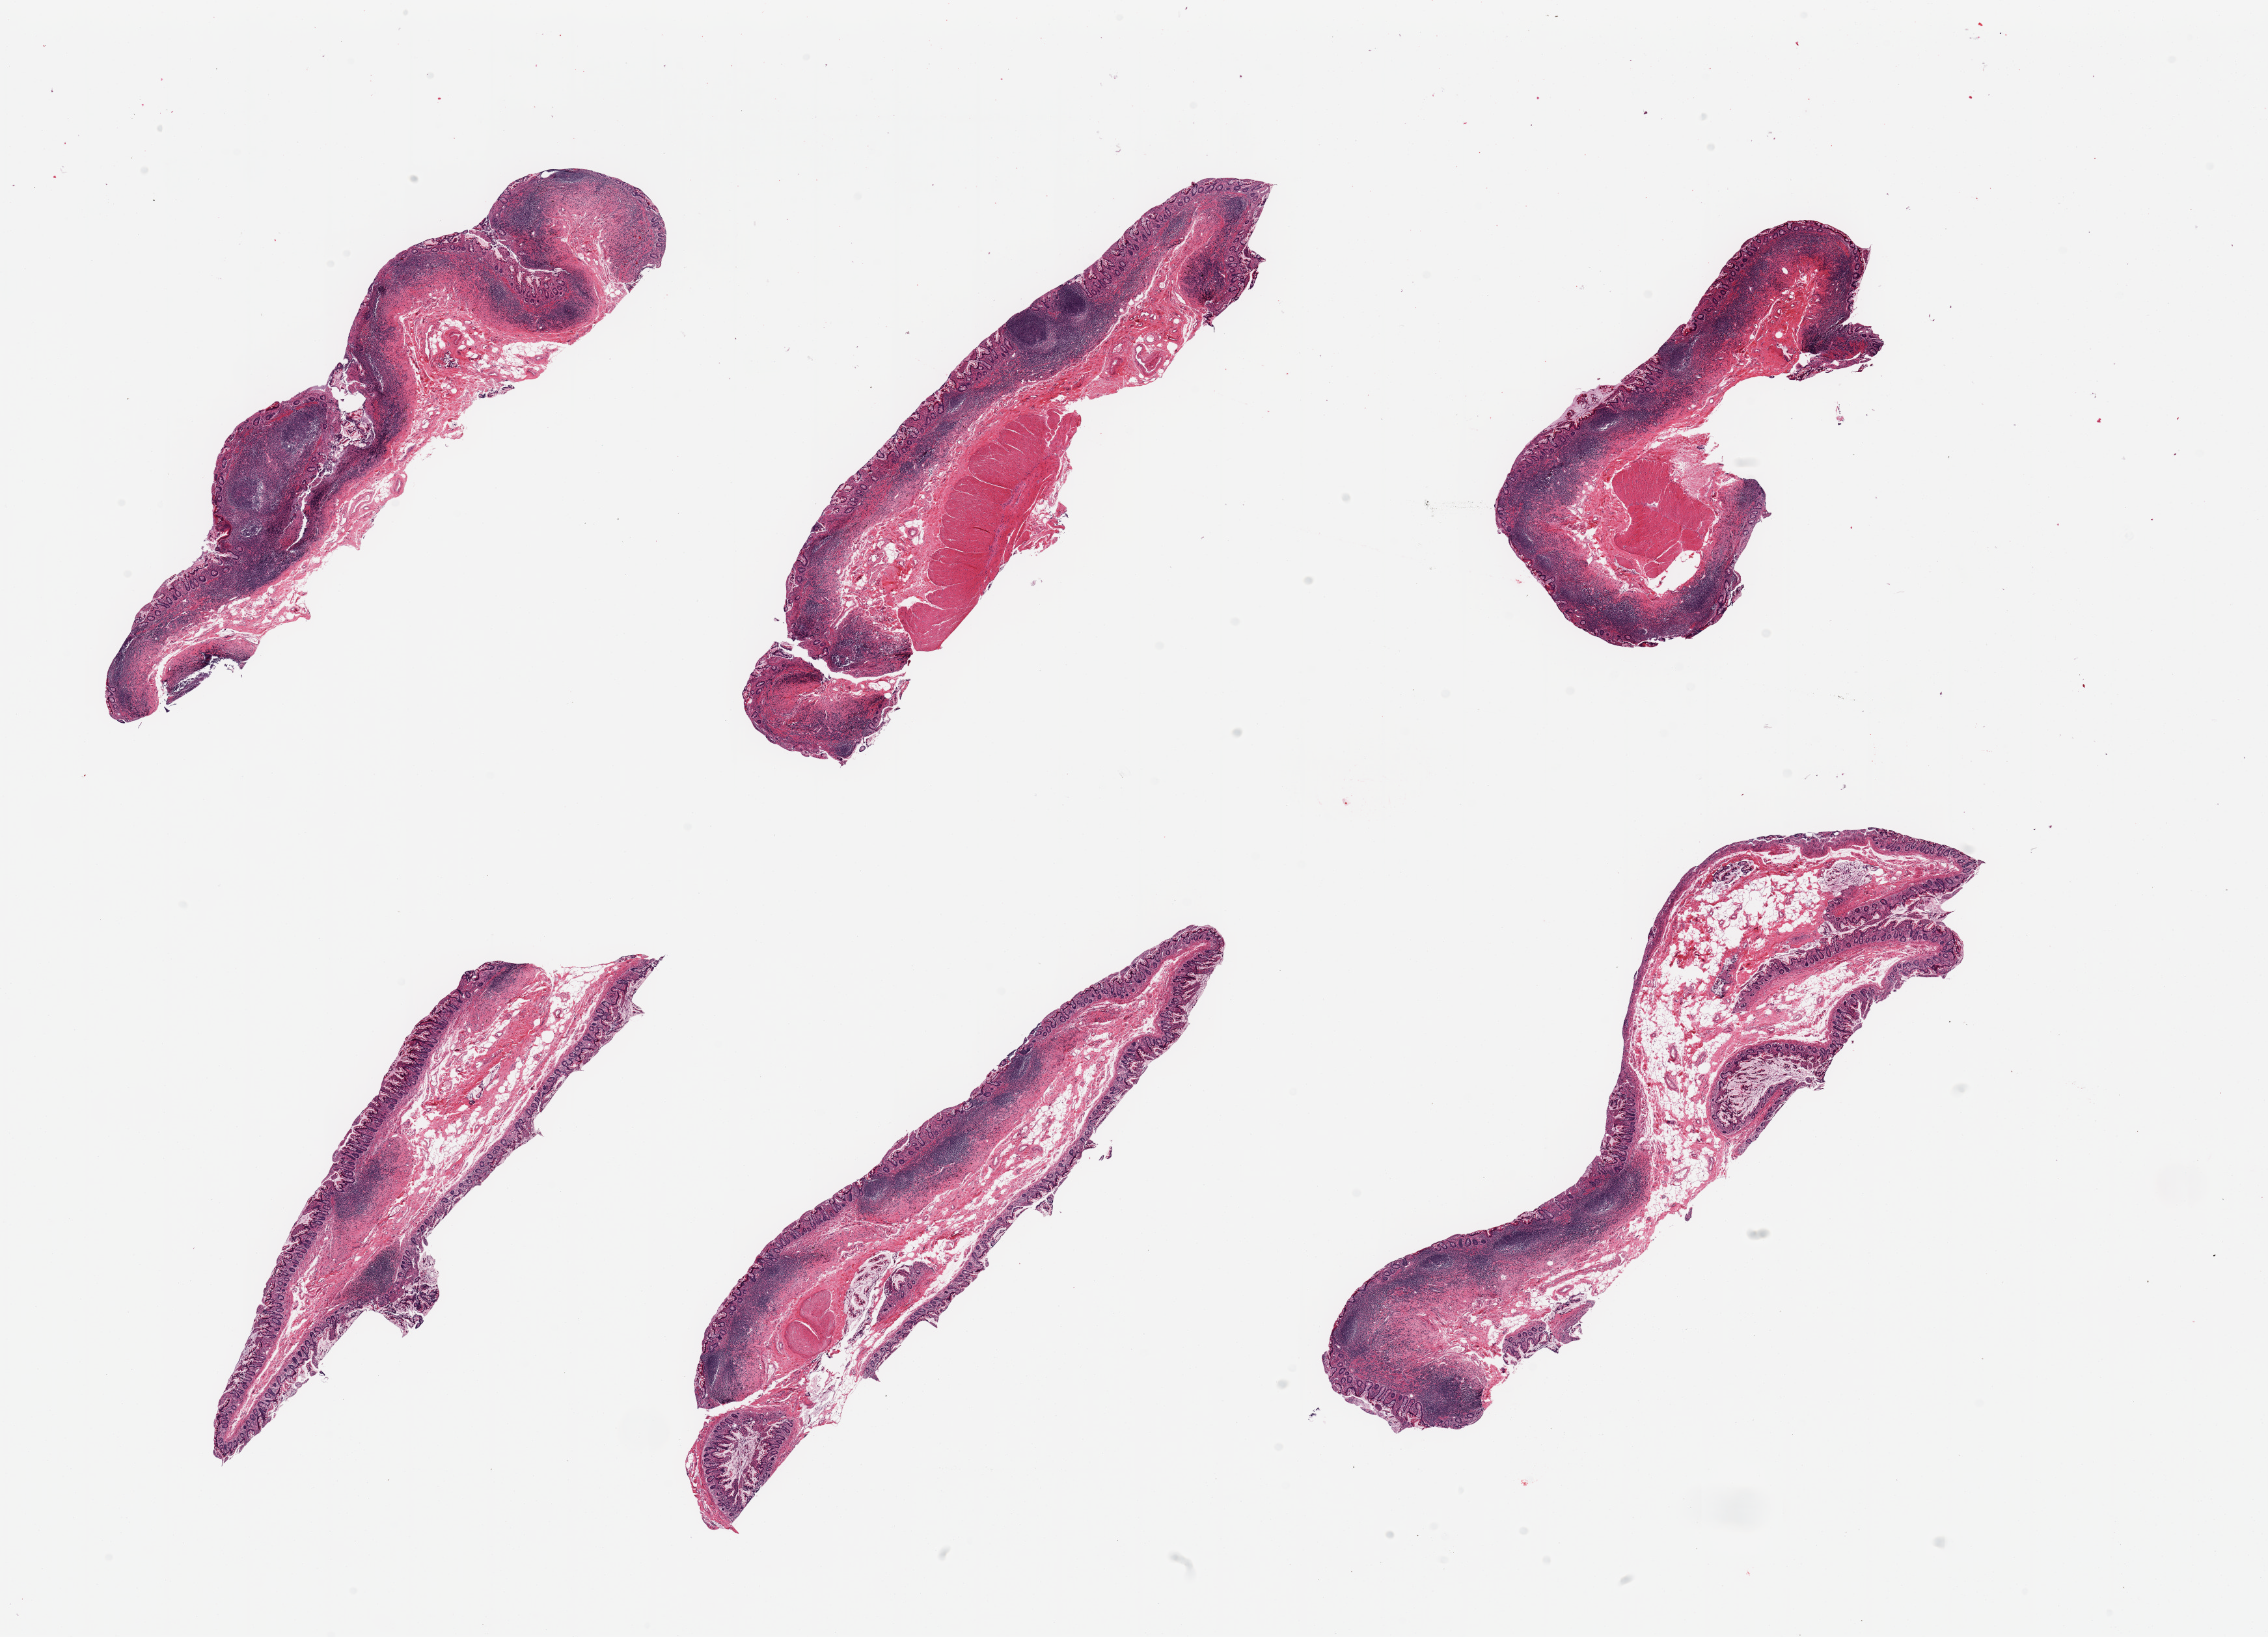
Haematoxylin and eosin whole-slide image — low-resolution overview of the scanned area, about 27.6 x 19.9 mm; PAXgene-fixed paraffin-embedded (PFPE) section; section of ileum (target tissue); tissue donor sample. Donor sex: male.
Pathologist's review note for this sample: 6 pieces, target lymphoid aggregates are ~30-40% of tissue.